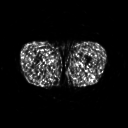
FDG PET of an extremity soft-tissue mass (from a PET/CT study), one axial slice; position 223 of 267 along the scan axis; 3.27 mm slice thickness; 128 × 128 image matrix. Male patient, age 27 years. From the clinical record (not read from this slice): histological type: extraskeletal osteosarcoma; grade: high; site of the primary tumour: left adductur.
Structures marked on this image (expert contour drawn on MRI and transferred to this co-registered scan by the dataset authors):
- gross tumour volume (mass): box from (x=70, y=62) to (x=91, y=72) px